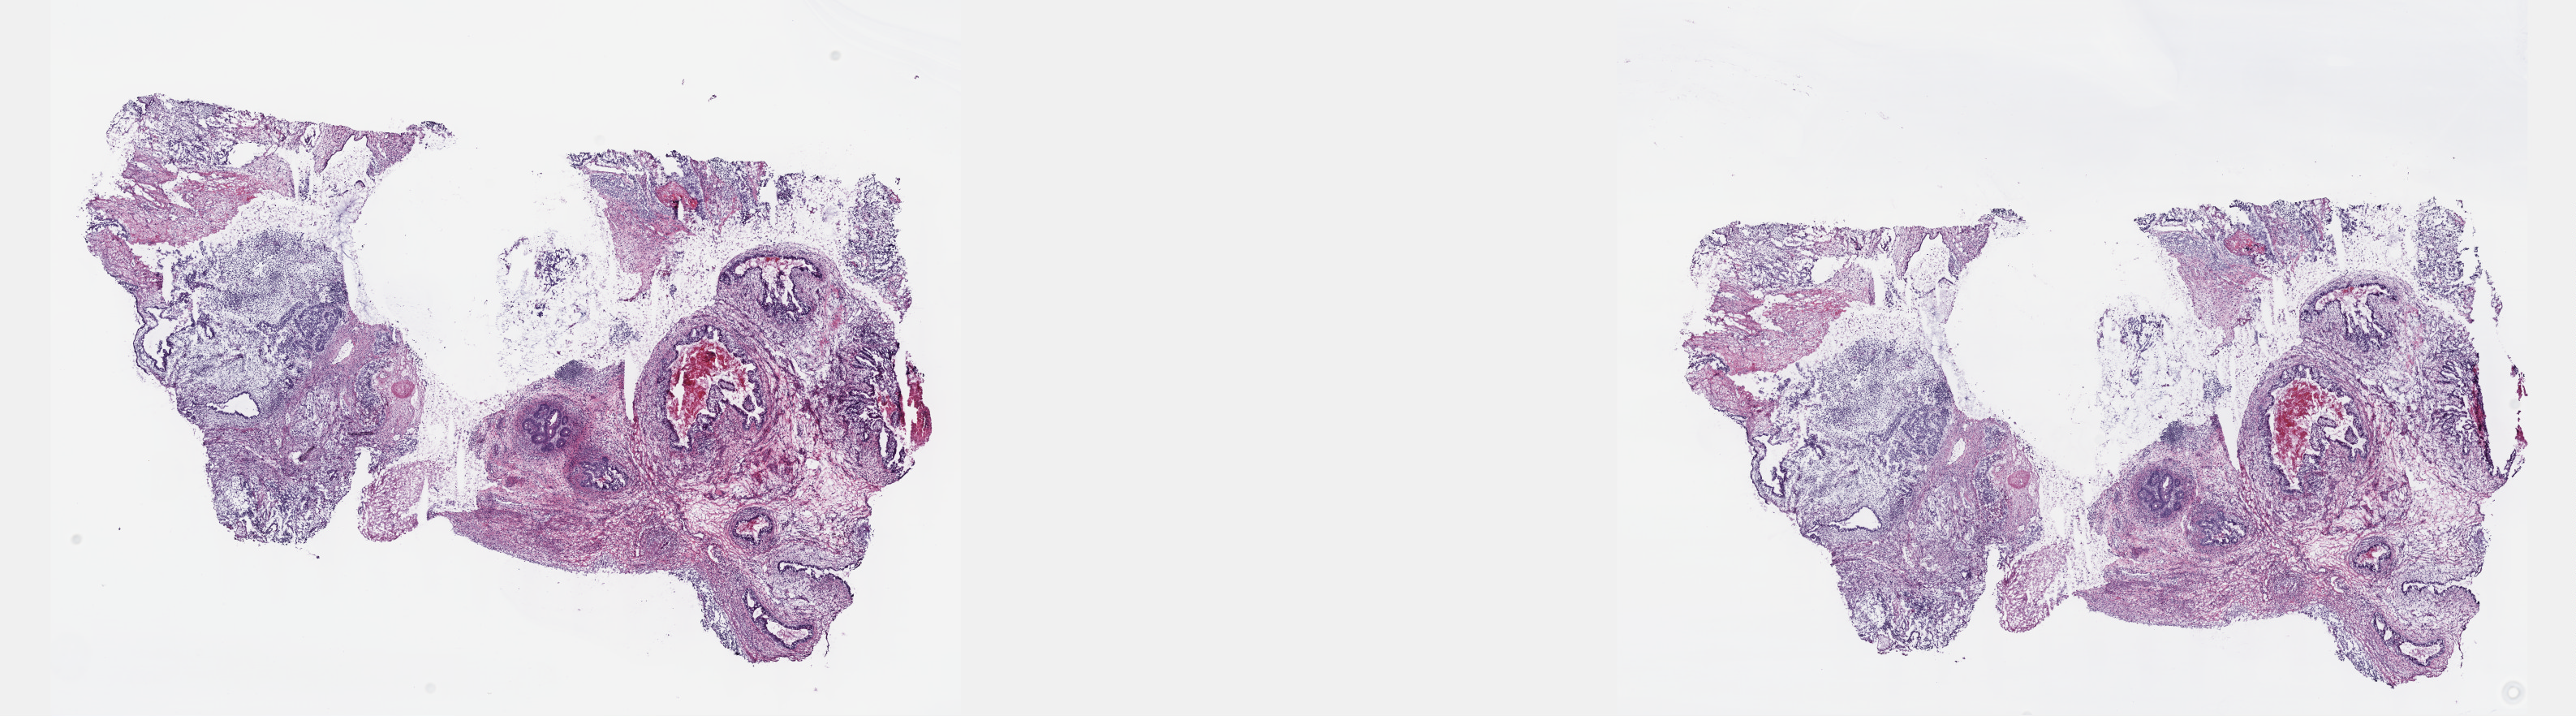
Digitized H&E tissue section (whole slide), whole scanned area (about 25.7 x 7.1 mm, slide scanned at 40x) shown as a low-resolution overview. Frozen section from the top of the tissue portion. Sample: primary tumour, testis. Male patient; age at initial diagnosis 20 years. Pathologist review of this section (percent, as recorded): tumour cells 75%, tumour nuclei 75%, normal cells 0%, stromal cells 20%, necrosis 5%. Inflammatory infiltration, as recorded: lymphocyte infiltration 2%, monocyte infiltration 1%, neutrophil infiltration 2%.
TNM: T3 N1 M1b. Histologic diagnosis: Mixed germ cell tumor. AJCC pathologic stage: IIIC.